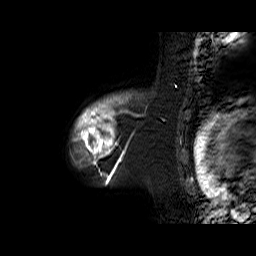
Breast MRI (dynamic contrast-enhanced), one sagittal slice. Position 53 of 60 along the scan axis. Dynamic contrast-enhanced series, time point 2 of 6 at this slice position (early post-contrast). 1.5 T. TE 6.3 ms, TR 32.9 ms. 4 mm slice thickness. 256 × 256 image matrix, field of view 200 × 200 mm. Female patient. Case-level facts recorded for this patient, not image findings: setting: breast cancer imaged before/during neoadjuvant chemotherapy; receptor status: triple-negative.
Structures marked on this image (semi-automatically segmented with operator editing):
- analysis volume of interest (the breast-tissue region the enhancement analysis was run in; not a lesion): bounding box <72,95,143,170> (left, top, right, bottom; pixels)
- tumour enhancement mask (voxels above the 100 % enhancement threshold inside the analysis volume of interest): <72,95,128,170>